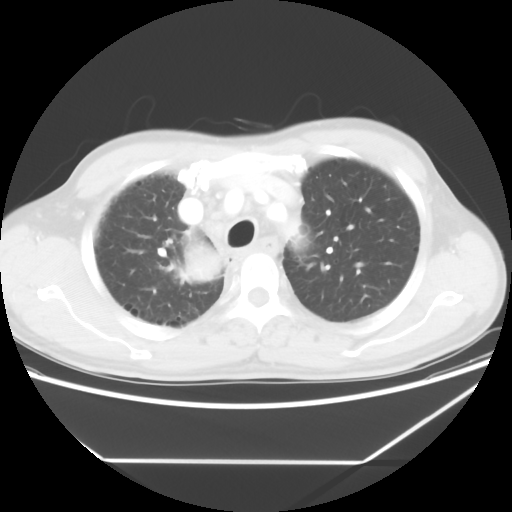
Chest CT, one axial slice; position 47 of 60 along the scan axis; reconstruction kernel STANDARD; 120 kVp; lung window (W 1500 / L -600 HU); 5 mm slice thickness; 512 × 512 image matrix. Patient: male, 58 years. From the clinical record (not read from this slice): clinical TNM (as recorded): T2 N2 M0.
Structures marked on this image (rectangle marked by the reading radiologist):
- lung tumour (recorded histology: squamous cell carcinoma): bounding box <174,241,228,292> (left, top, right, bottom; pixels)